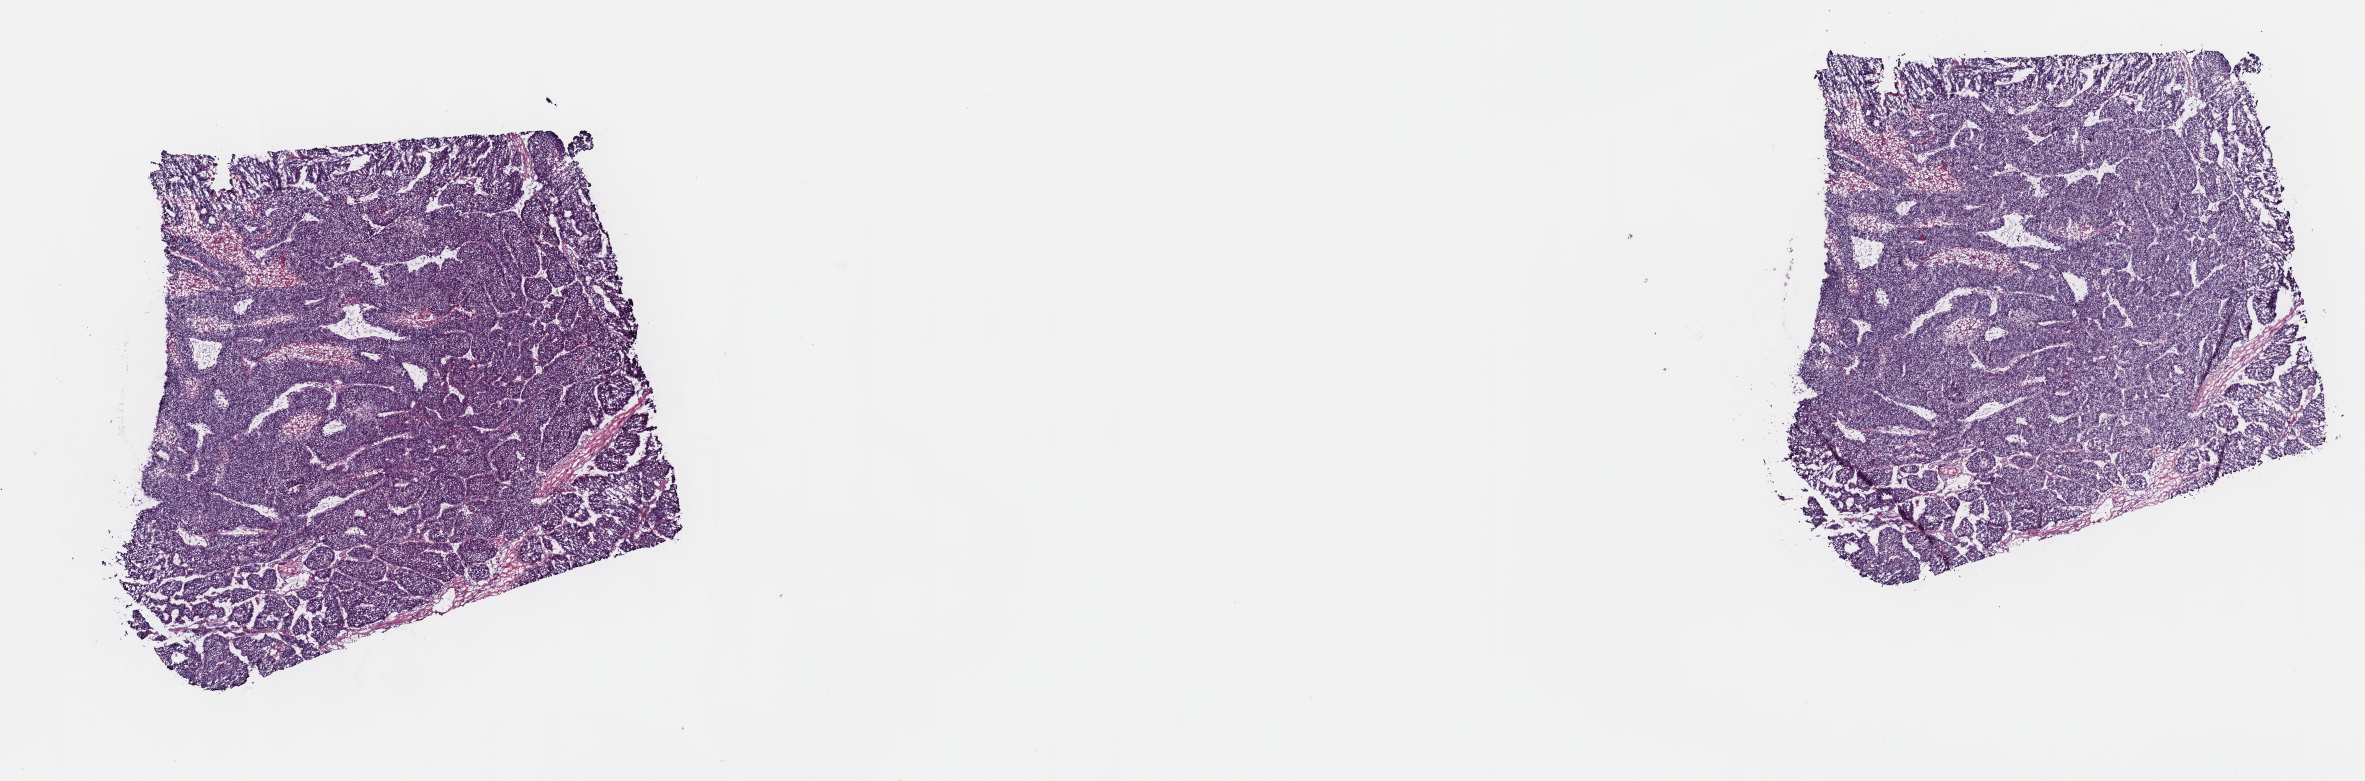
H&E whole-slide image, shown as a low-resolution overview of the whole scanned area (about 19.1 x 6.3 mm); frozen section from the top of the tissue portion; primary tumour sample from the liver. Female, age 52 years at initial diagnosis.
Diagnosis: Hepatocellular carcinoma, NOS.